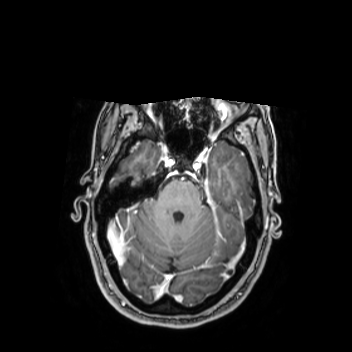
Brain MRI from a brain-tumour surgery series, one axial slice; slice 176 of 350 in the series (ordered by position); T1-weighted post-contrast; 0.9 mm slice thickness; 352 × 352 image matrix, field of view 280 × 280 mm. Case-level facts recorded for this patient, not image findings: histopathology: Oligodendroglioma; WHO grade: 2; IDH mutation: yes; tumour location: Left Middle Temporal Gyrus.
Annotated regions visible in this slice (outlined manually by an expert reader):
- tumour: bounding box (x1, y1, x2, y2) in pixels: (224, 171, 262, 199)